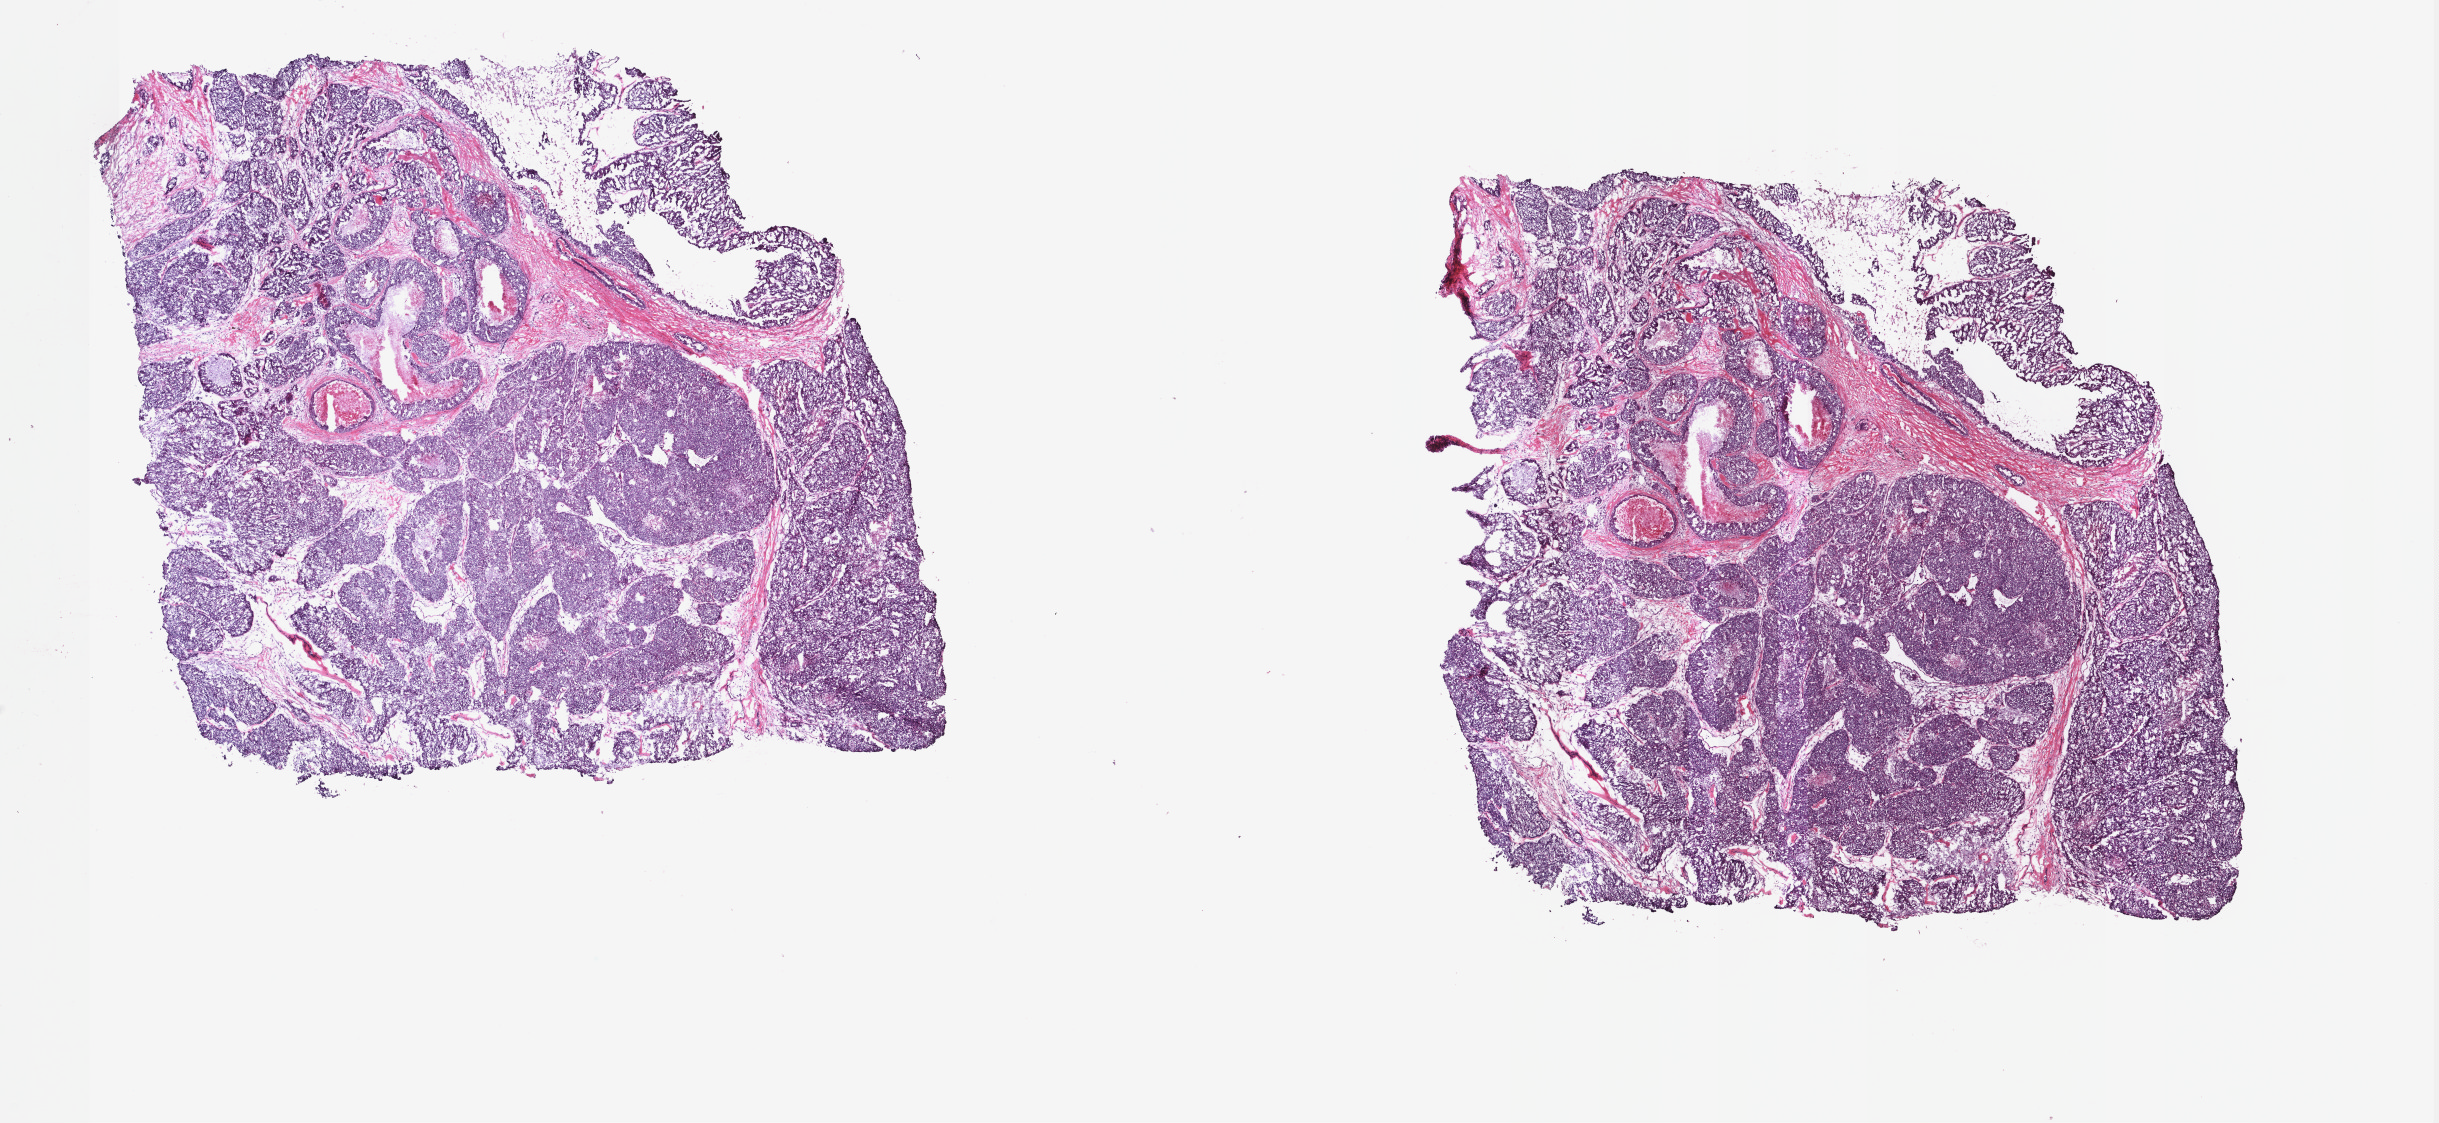
Hematoxylin and eosin (H&E) stained whole-slide image, low-resolution overview of the scanned area, about 19.4 x 8.9 mm (acquisition: 40x scan); frozen section from the top of the tissue portion; sample: primary tumour, breast. Female patient; age at initial diagnosis 70 years. Pathologist review of this section (percent, as recorded): tumour cells 70%, tumour nuclei 80%, normal cells 0%, stromal cells 20%, necrosis 10%. Inflammatory infiltration, as recorded: lymphocyte infiltration 0%, monocyte infiltration 0%, neutrophil infiltration 0%.
Lymph nodes positive (case pathology): 0 of 15 examined. Pathologic diagnosis: Infiltrating duct mixed with other types of carcinoma. AJCC pathologic stage: IIA (7th edition).